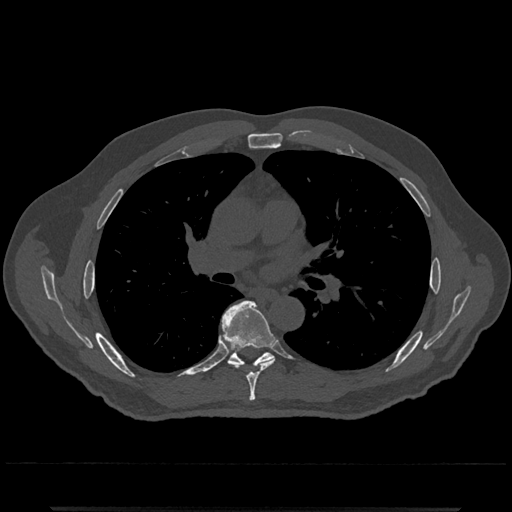
CT including the spine, one axial slice; slice 752 of 797 in the series (ordered by position); bone window (W 1800 / L 400 HU); 0.5 mm slice thickness; 512 × 512 image matrix, field of view 393 × 393 mm. Patient: male, 67 years. Case-level facts recorded for this patient, not image findings: primary cancer: prostate.
Outlined on this slice (semi-automatic segmentation, software-assisted and operator-edited):
- T6 vertebra: bounding box (x1, y1, x2, y2) in pixels: (221, 300, 275, 401)
- T7 vertebra: (228, 346, 274, 368)